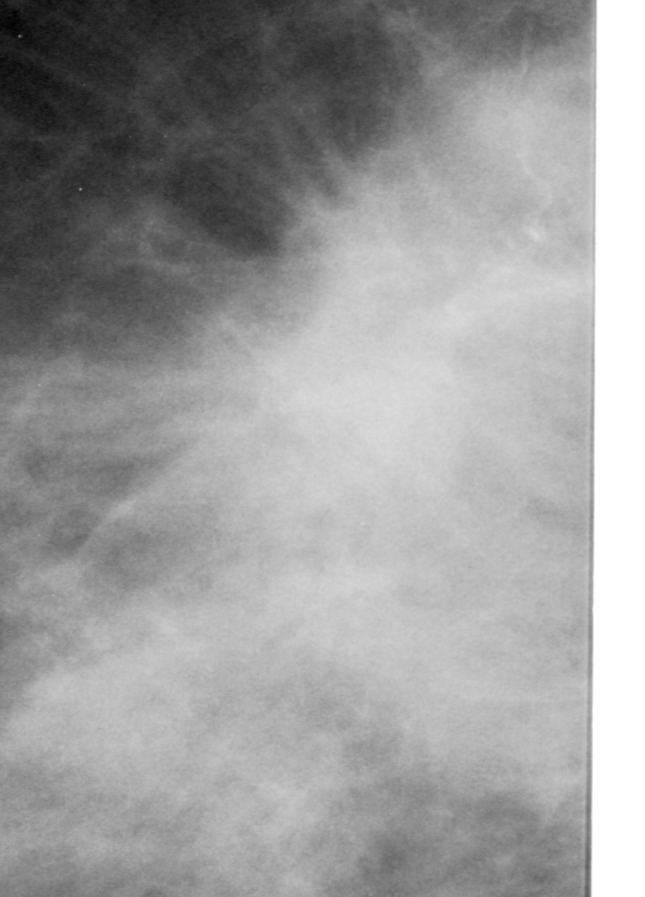
Cropped region of a digitized screen-film mammogram centred on a radiologist-marked abnormality, left breast, CC view.
Mass, shape irregular, margins spiculated; BI-RADS assessment category 5; subtlety rating 5 on a 1 (subtle) to 5 (obvious) scale; pathology result (as recorded, not read from the image): malignant.